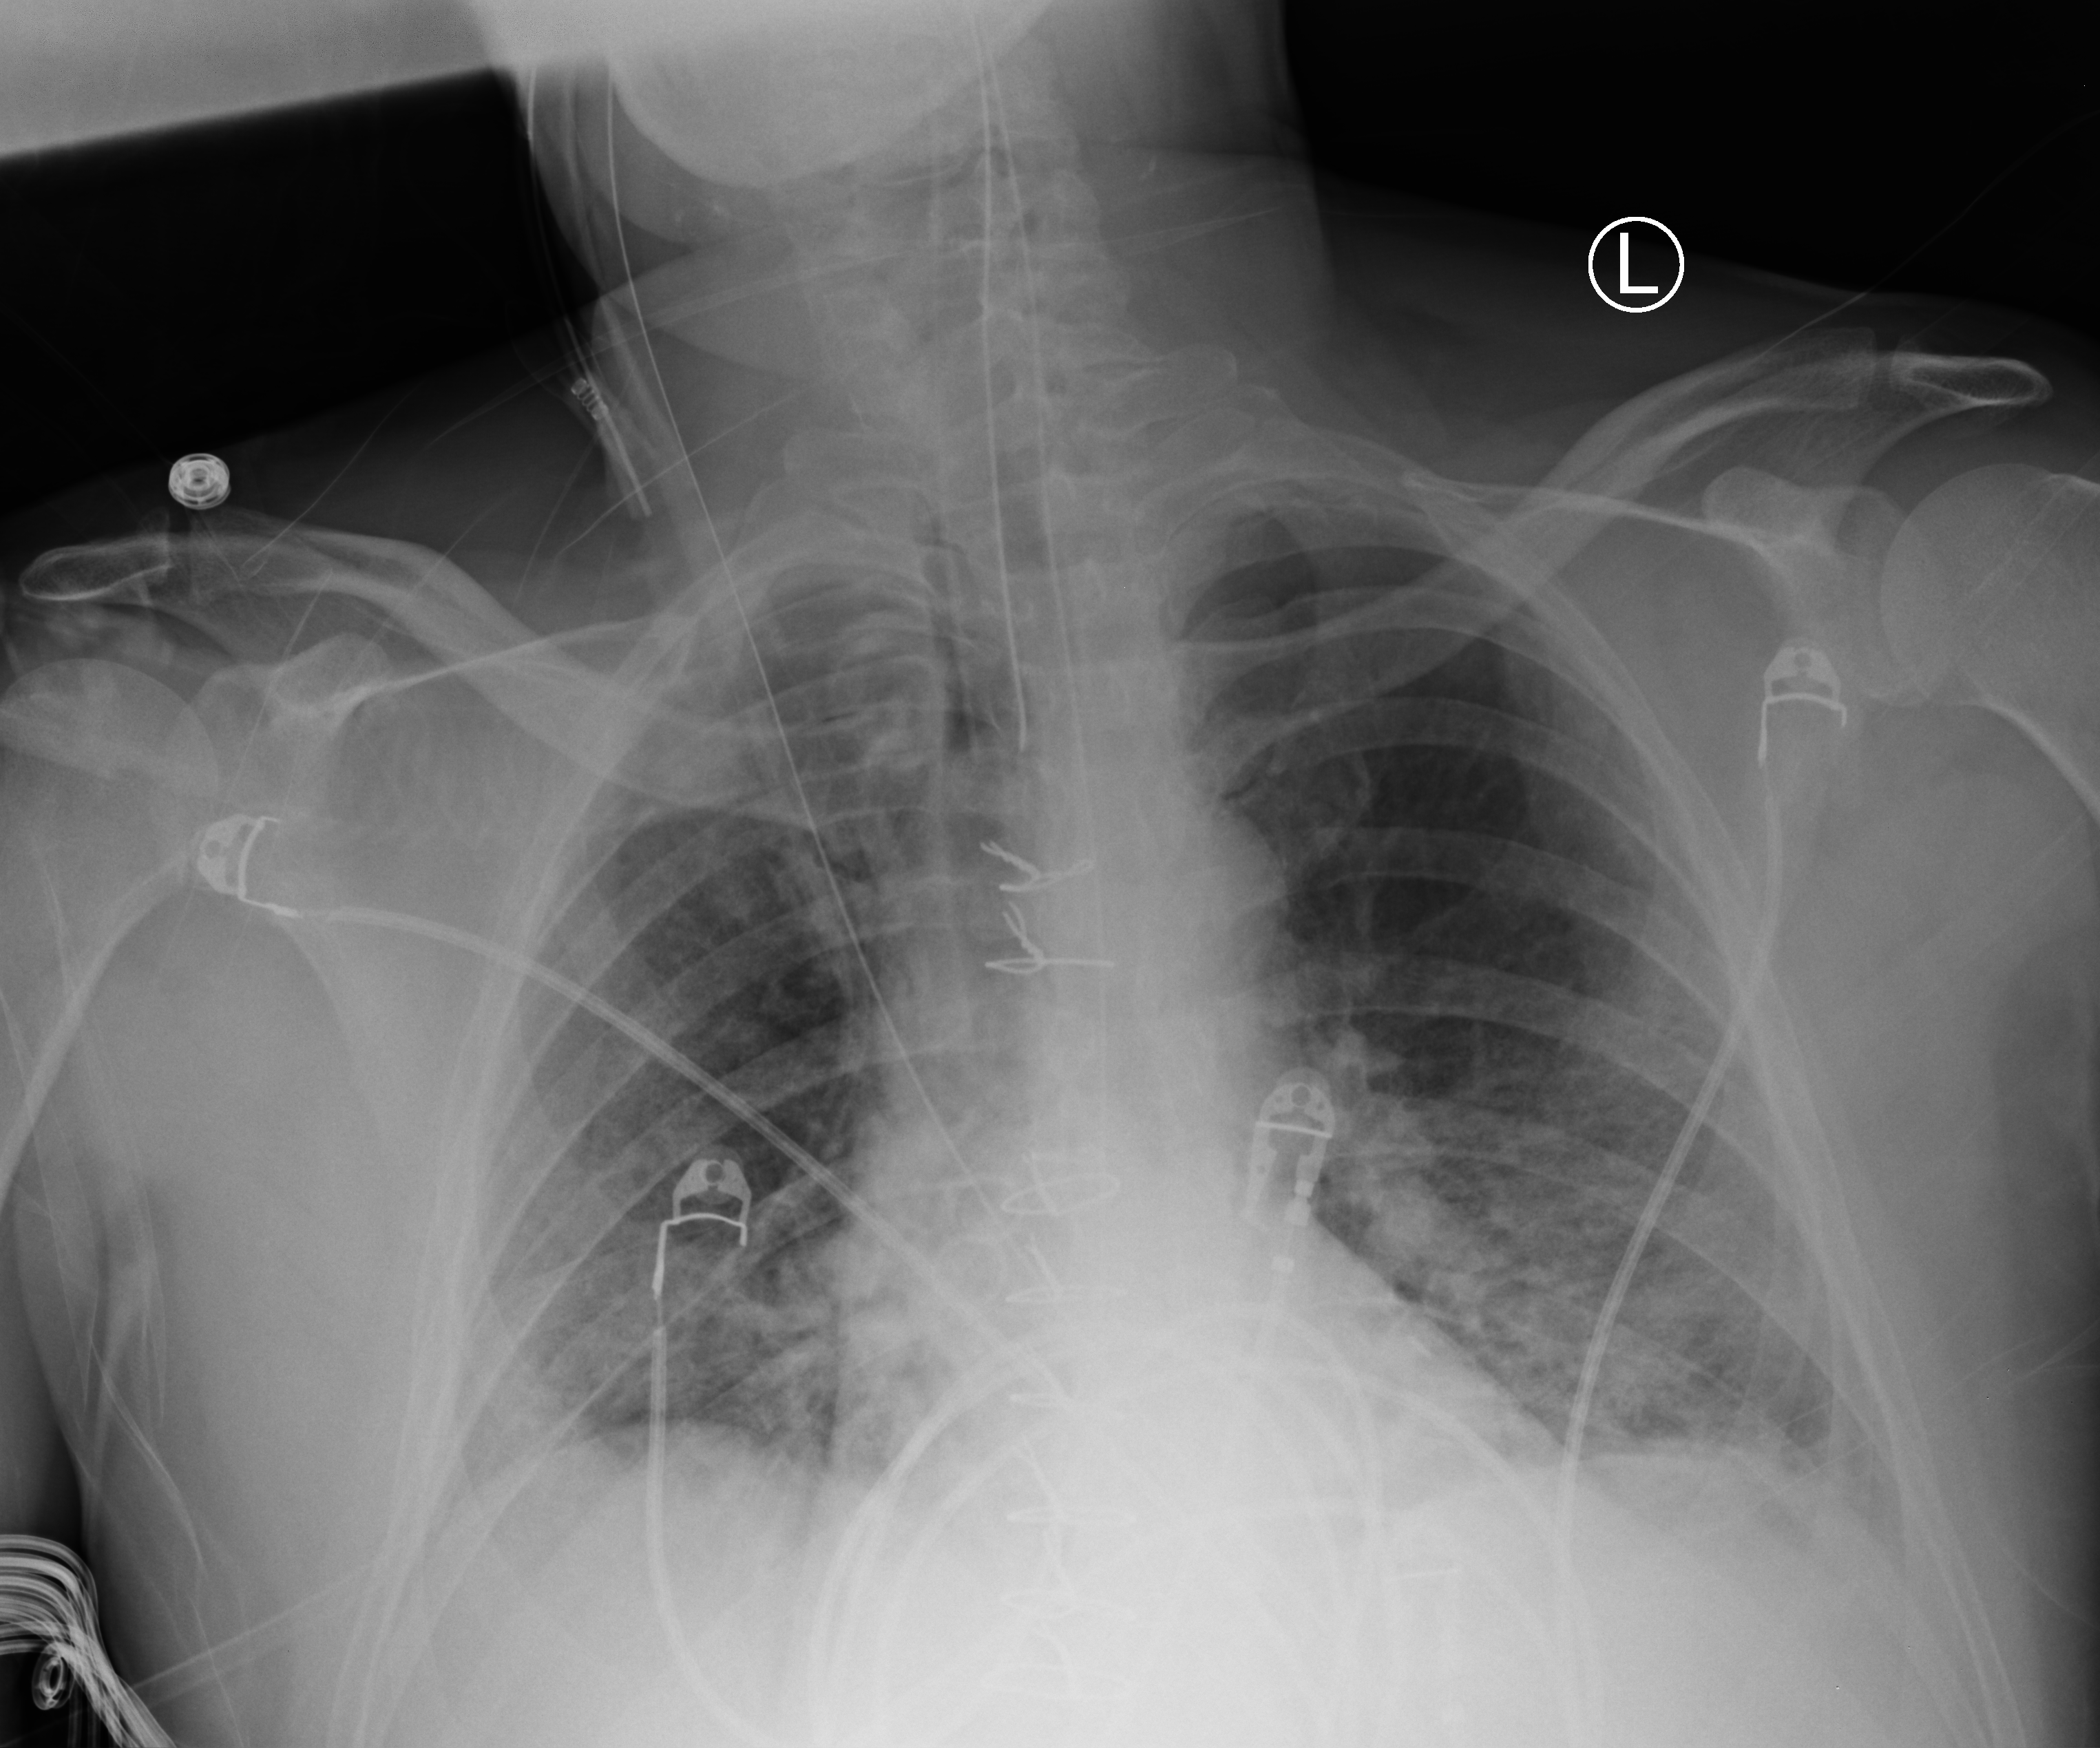
Chest X-ray (portable); anteroposterior (AP) projection. Male patient hospitalised with COVID-19, age 18–59 years.
From the hospital-stay record, not from the radiograph (when in the stay this image was taken is not recorded): mechanically ventilated during this hospital stay: yes; admitted to intensive care during this hospital stay: yes.